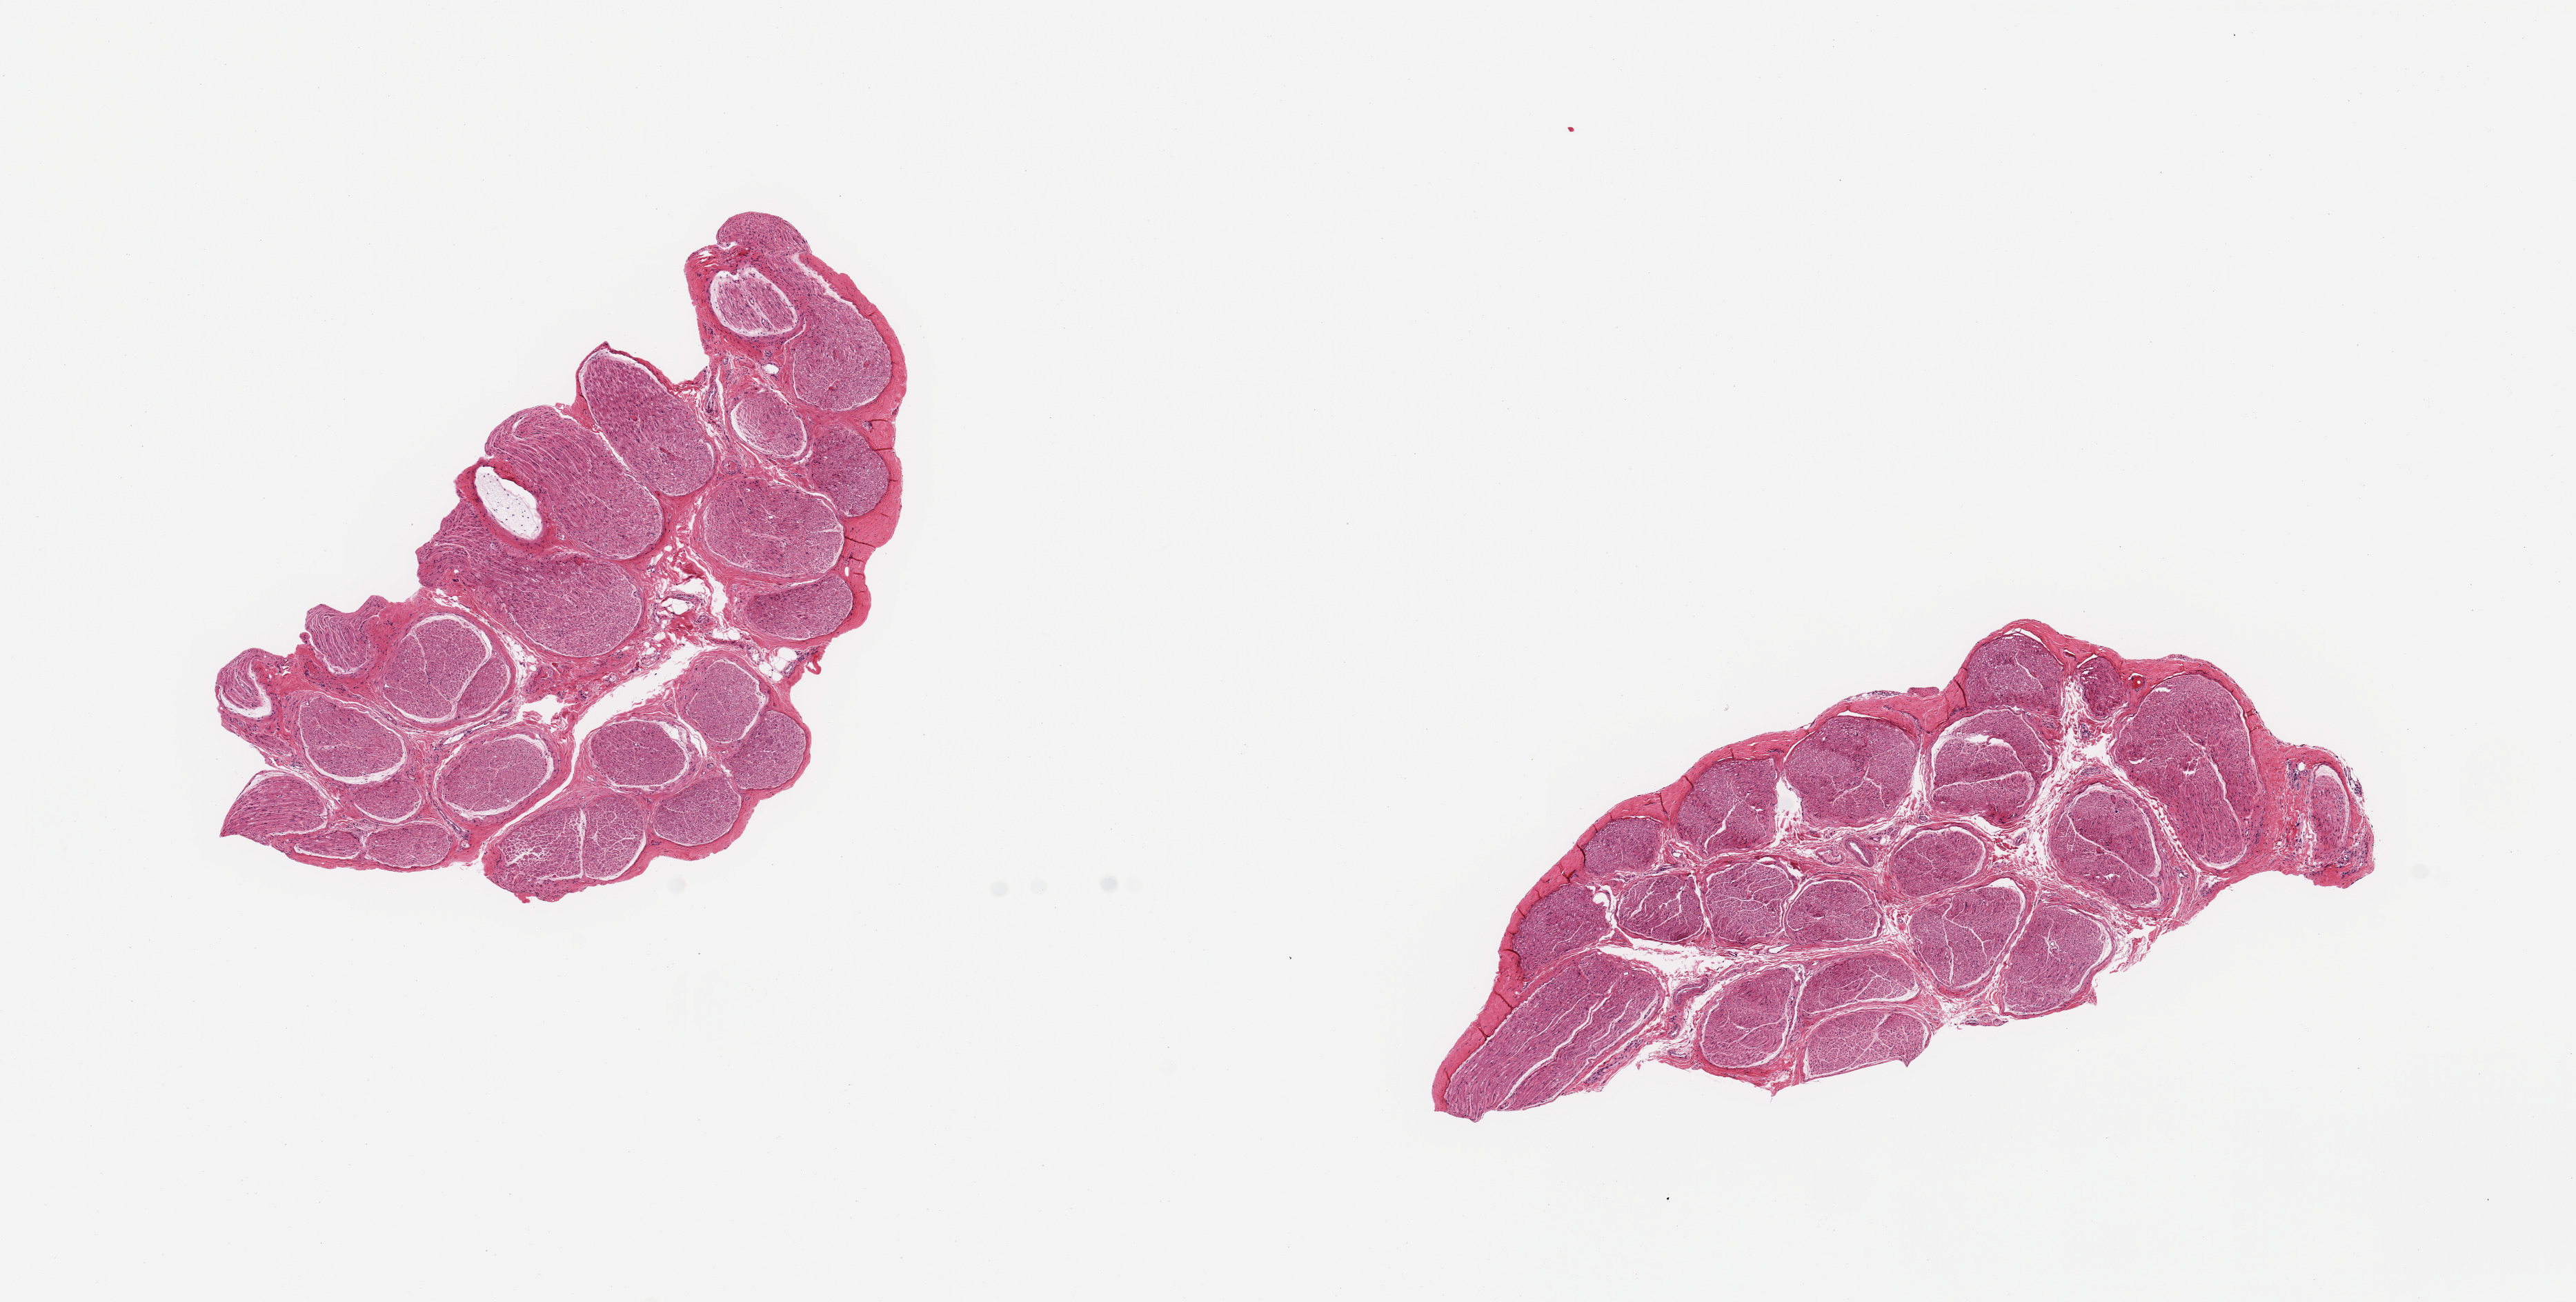
Whole-slide image, H&E stain, brightfield — a low-resolution overview of the entire scanned area, about 14.8 x 7.5 mm. PAXgene-fixed paraffin-embedded (PFPE) section. Target tissue: tibial nerve. Tissue donor sample. Donor: female.
Pathologist's review note for this sample: 2 pieces; well dissected with virtually no extraneous fat.